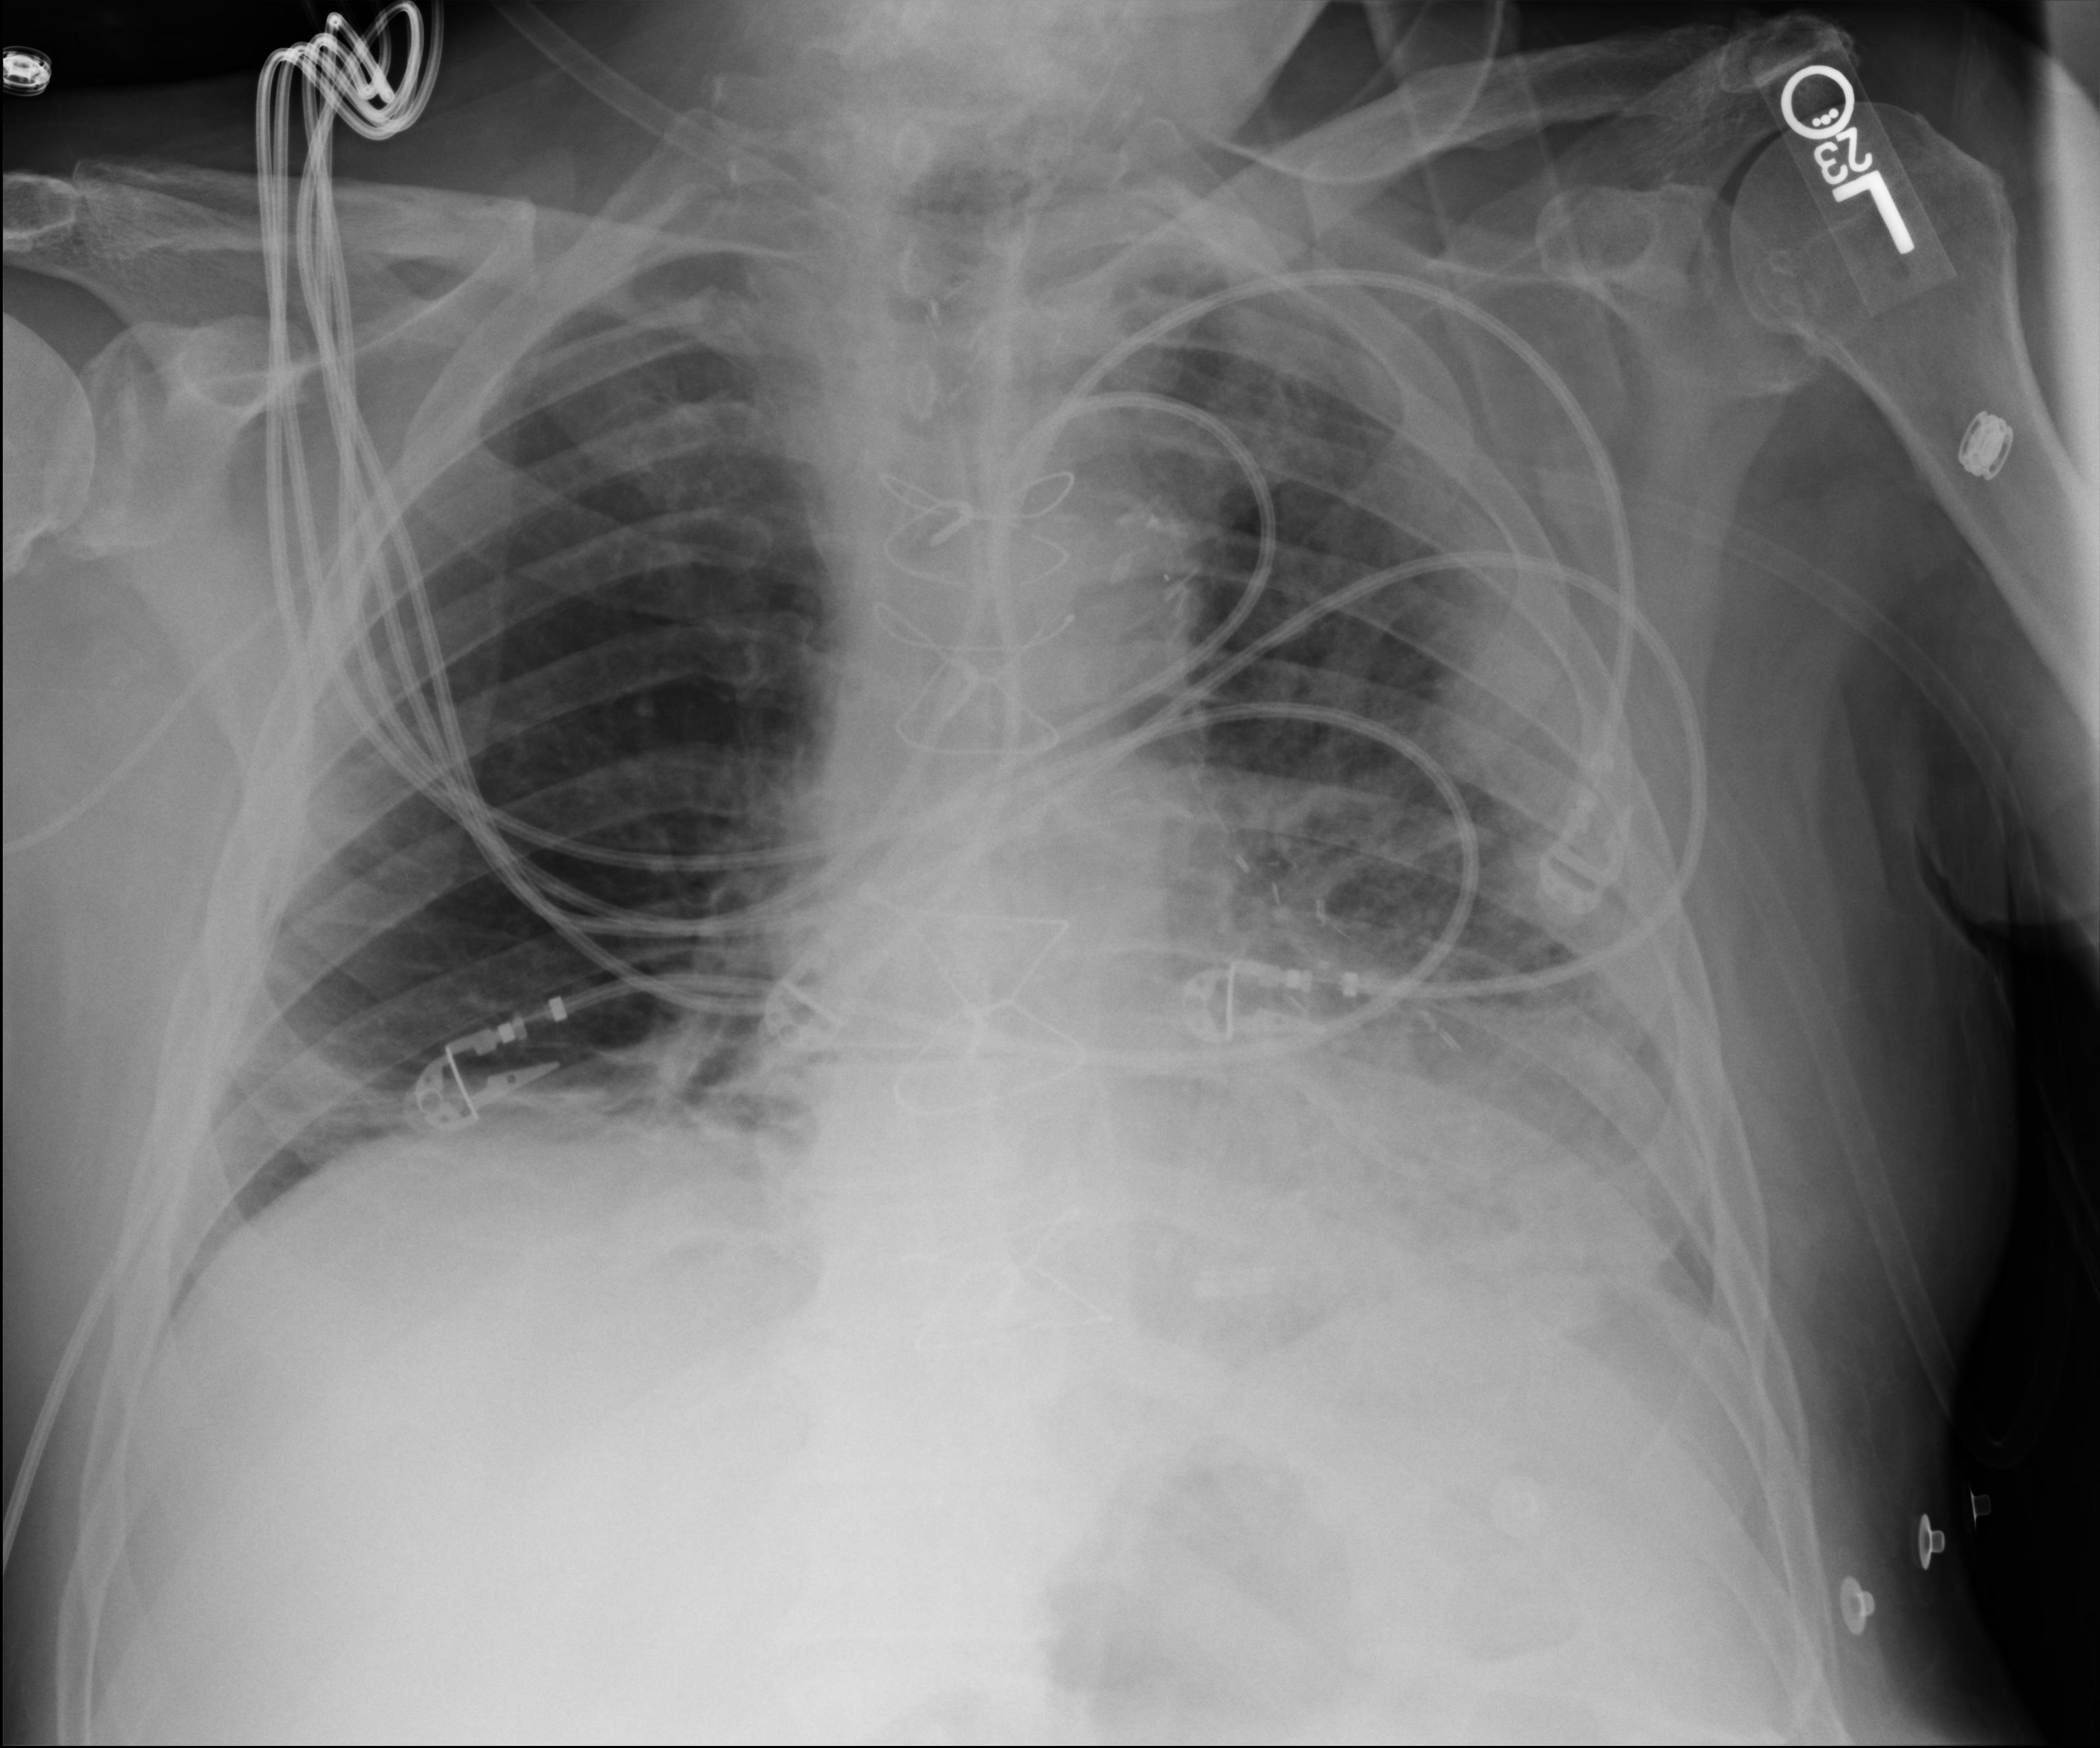
Portable chest radiograph, anteroposterior (AP) projection. Male patient hospitalised with COVID-19, age 60–74 years.
Hospital-stay facts (about this admission, not read from this image; timing relative to this image not recorded): admitted to intensive care during this hospital stay: yes; other chronic lung disease (admission record): no.